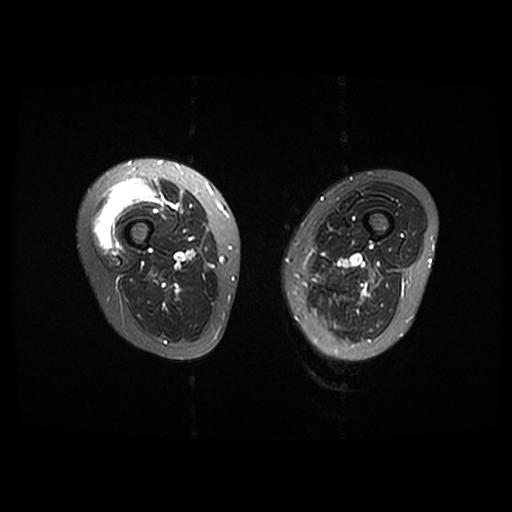
MRI of an extremity soft-tissue mass, one axial slice; slice 7 of 42 in the series (ordered by position); T2-weighted fat-saturated; 512 × 512 image matrix, field of view 440 × 440 mm. Female patient. From the clinical record (not read from this slice): histological type: pleiomorphic undifferentiated sarcoma; grade: high; site of the primary tumour: right quadricep.
Structures marked on this image (outlined manually by an expert reader):
- gross tumour volume including surrounding oedema: bounding box [x1, y1, x2, y2] px = [94, 178, 155, 250]